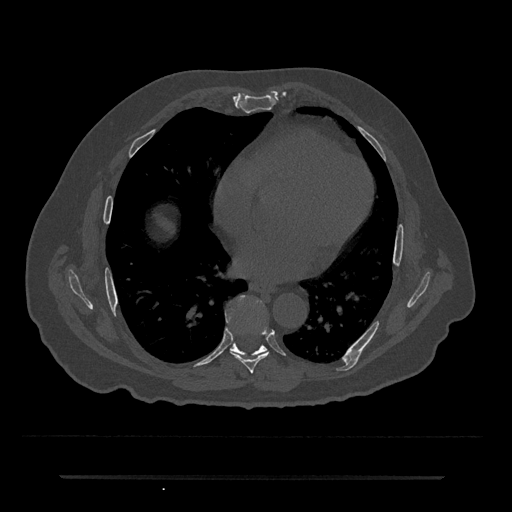
CT including the spine, one axial slice; position 364 of 797 along the scan axis; reconstruction kernel Br40s/3; bone window (W 1800 / L 400 HU); 0.5 mm slice thickness; 512 × 512 image matrix, field of view 437 × 437 mm. Male patient, age 69 years. Case-level facts recorded for this patient, not image findings: primary cancer: prostate.
Annotated regions visible in this slice (semi-automatically segmented with operator editing):
- T7 vertebra: bounding box <227,318,269,373> (left, top, right, bottom; pixels)
- T8 vertebra: <230,302,267,355>